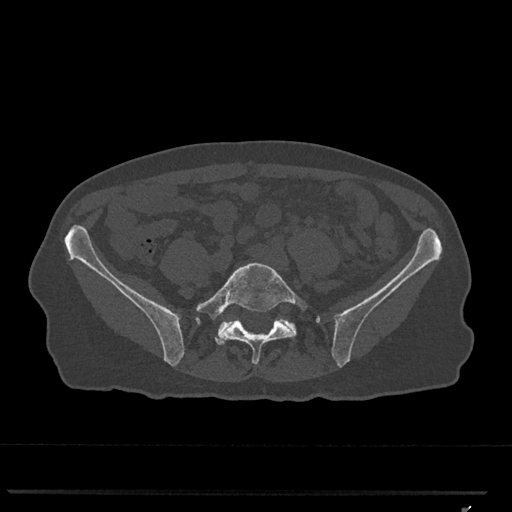
CT including the spine, one axial slice. Slice 144 of 793 in the series (ordered by position). Reconstruction kernel Br40s/3. 120 kVp. Bone window (W 1800 / L 400 HU). 0.5 mm slice thickness. 512 × 512 image matrix, field of view 380 × 380 mm. Patient: female, 62 years. From the clinical record (not read from this slice): primary cancer: renal.
Outlined on this slice (semi-automatic segmentation, software-assisted and operator-edited):
- L5 vertebra: bounding box <196,262,308,364> (left, top, right, bottom; pixels)